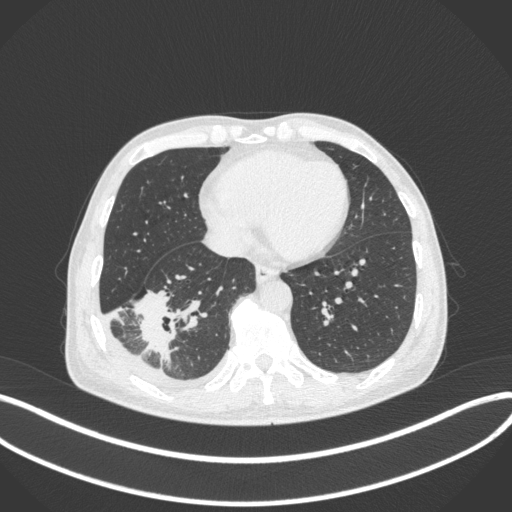
Chest CT, one axial slice; position 125 of 385 along the scan axis; reconstruction kernel B31f; 120 kVp; lung window (W 1500 / L -600 HU); 512 × 512 image matrix. Male patient, age 64 years. Case-level facts recorded for this patient, not image findings: clinical TNM (as recorded): T3 N0 M0; histopathological grade: G2-3.
Annotated regions visible in this slice (rectangle marked by the reading radiologist):
- lung tumour (recorded histology: adenocarcinoma): bounding box (x1, y1, x2, y2) in pixels: (130, 286, 173, 367)